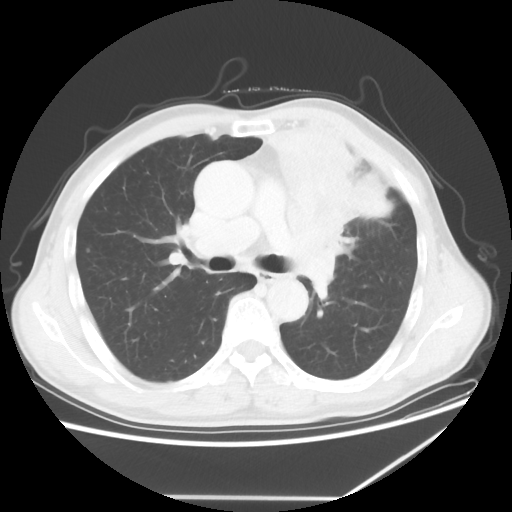
Chest CT, one axial slice; position 38 of 64 along the scan axis; reconstruction kernel STANDARD; 100 kVp; lung window (W 1500 / L -600 HU); 512 × 512 image matrix, field of view 383 × 383 mm. Patient: male, 64 years. Case-level facts recorded for this patient, not image findings: clinical TNM (as recorded): T1c N1 M1.
Annotated regions visible in this slice (rectangle marked by the reading radiologist):
- lung tumour (recorded histology: squamous cell carcinoma): bounding box [x1, y1, x2, y2] px = [257, 118, 416, 337]